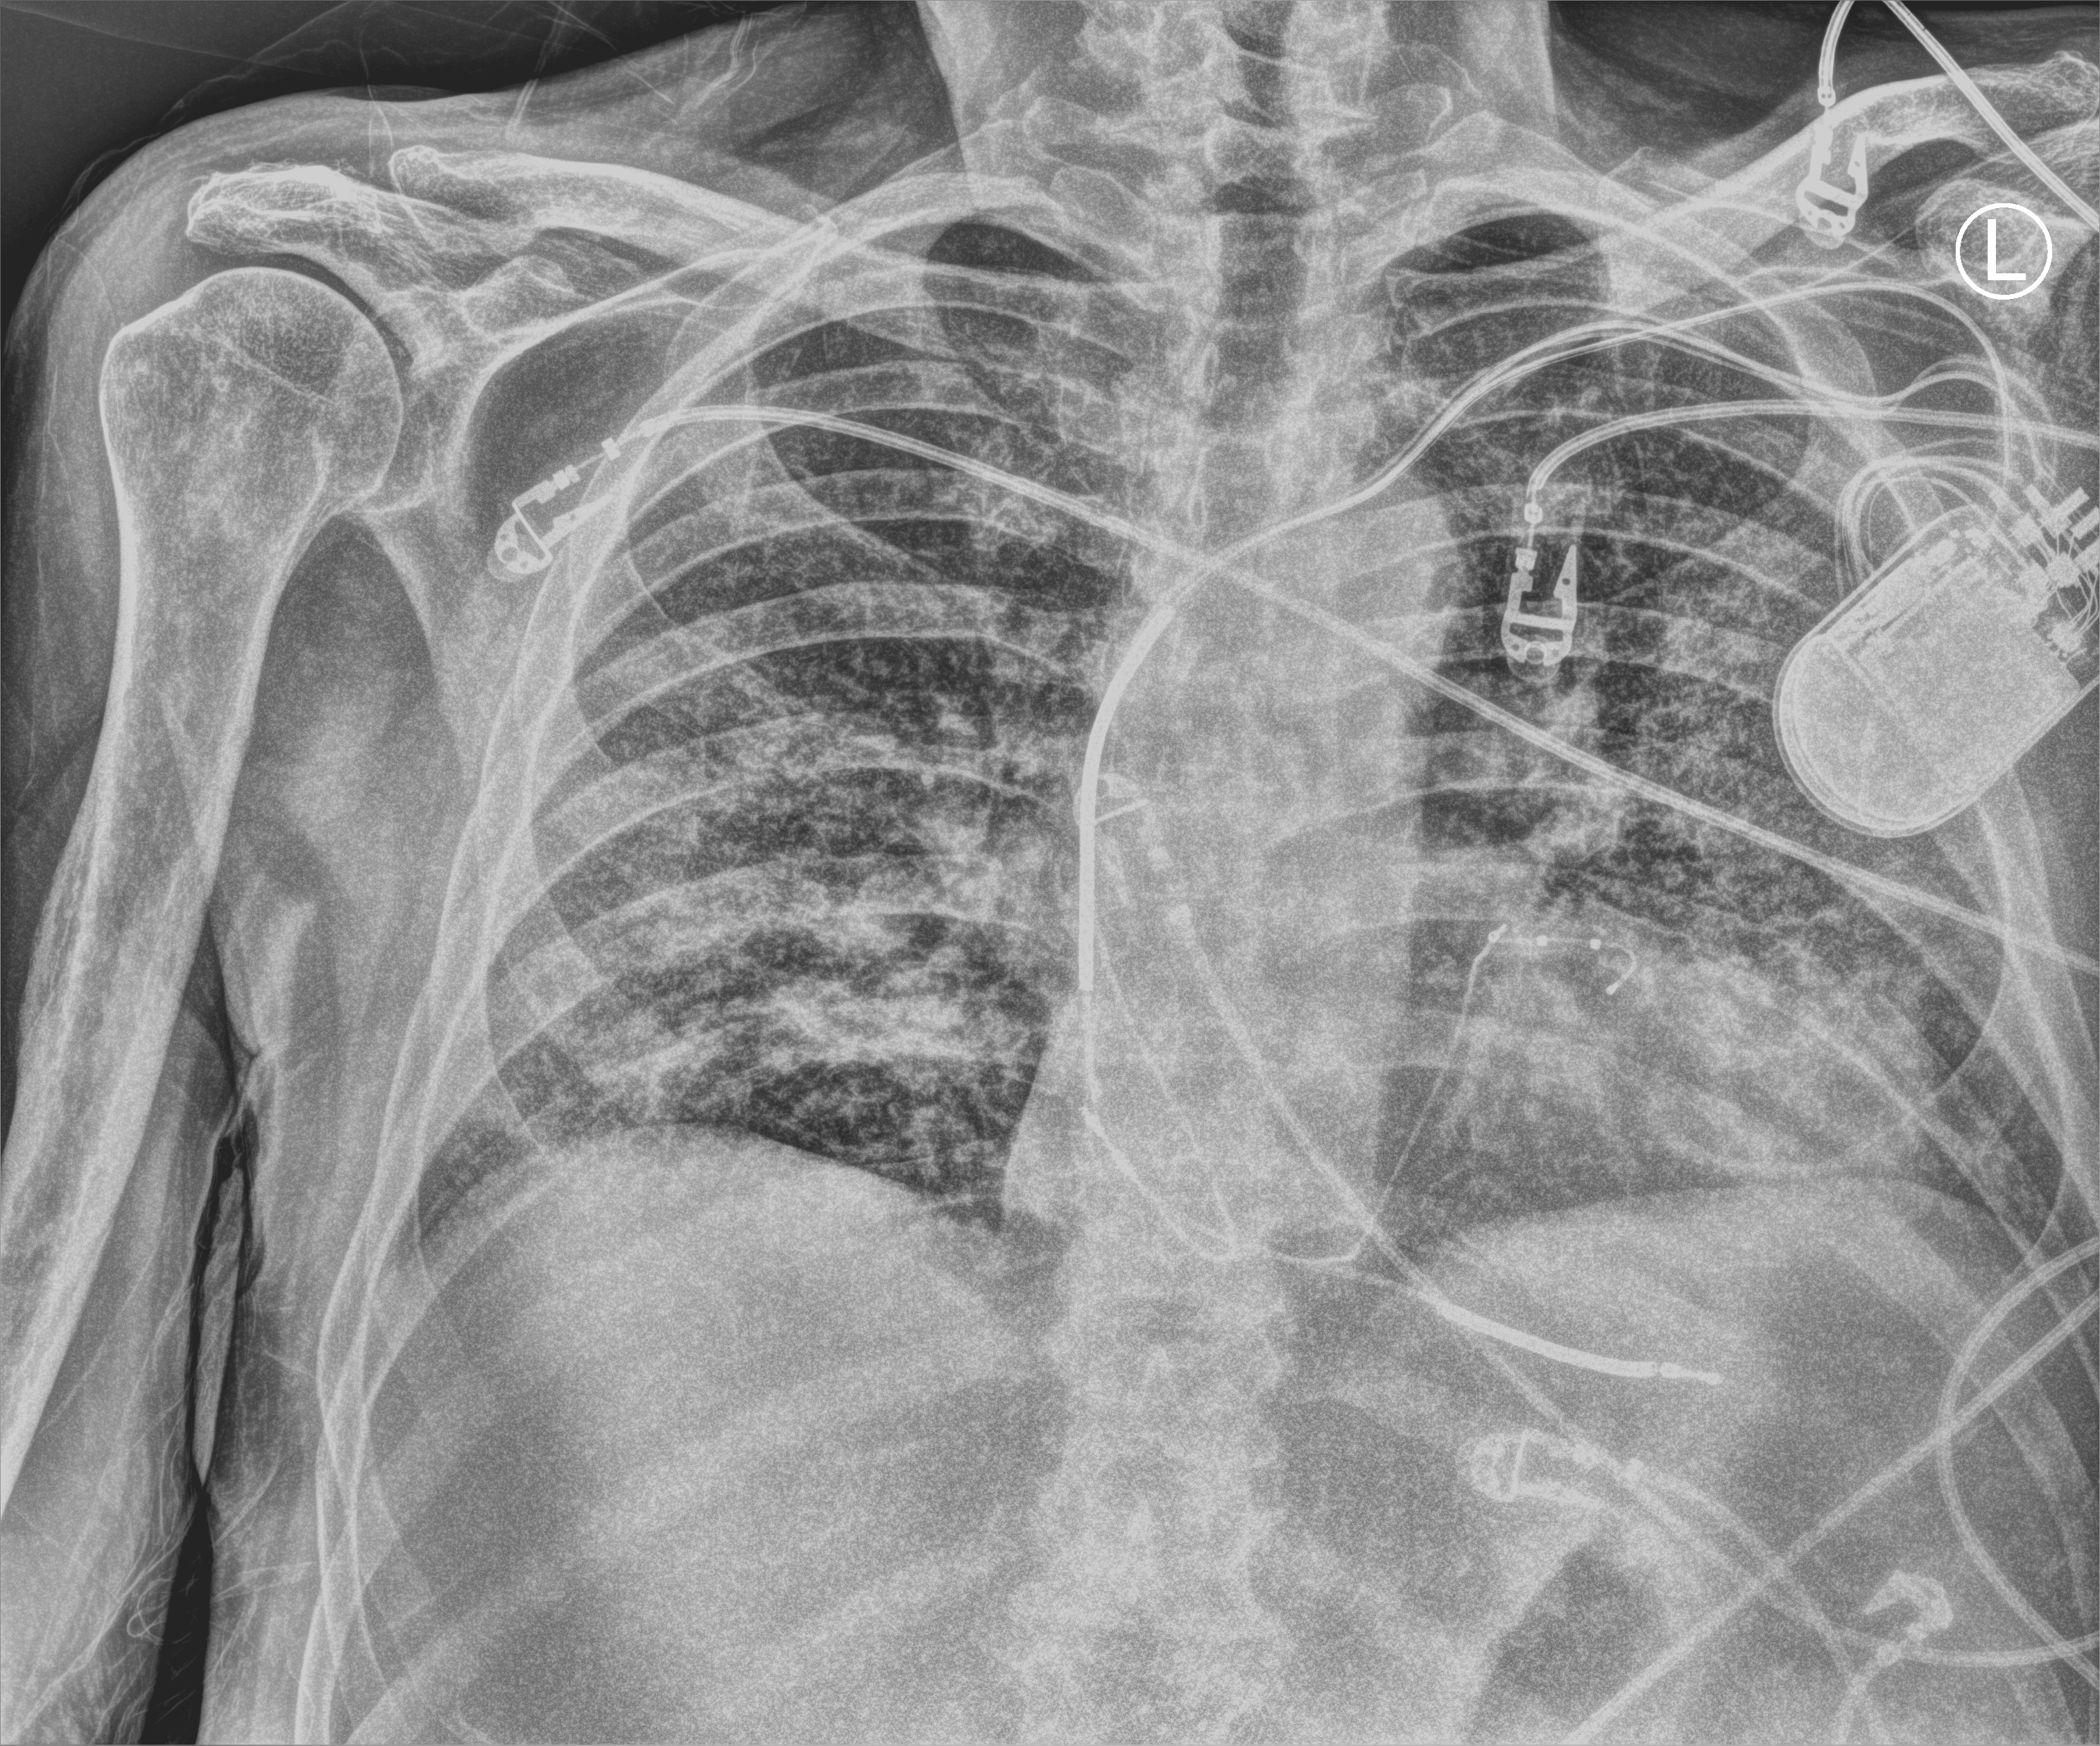
Portable chest radiograph. Patient hospitalised with COVID-19; male, aged 60–74 years.
Admission-level facts for this patient (not findings on this image; timing relative to this image not recorded): other chronic lung disease (admission record): no; admitted to intensive care during this hospital stay: yes; mechanically ventilated during this hospital stay: yes.